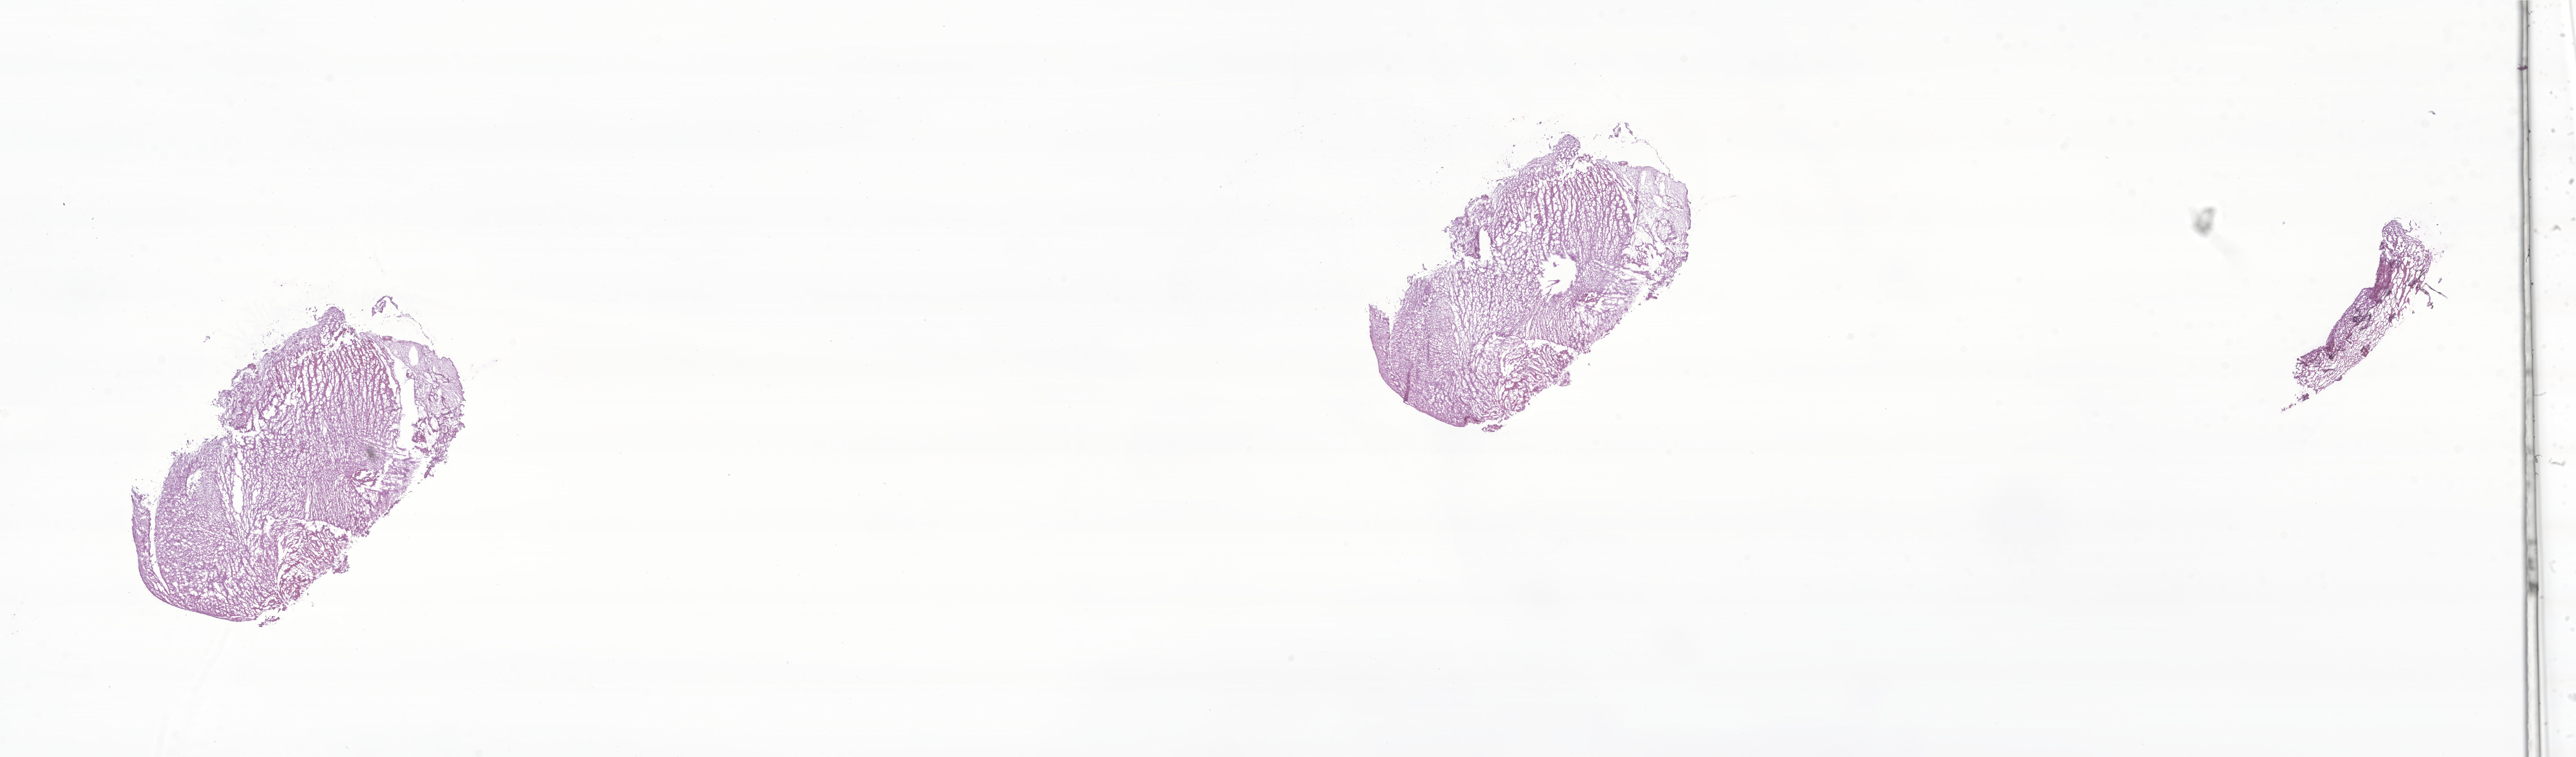
H&E whole-slide image of tumor tissue from the cerebellum — shown as a low-resolution overview of the whole scanned area (about 36.2 x 10.7 mm). Frozen section. Patient: male, age 212 months (17 years 8 months).
Diagnosis: Neoplasm, malignant.